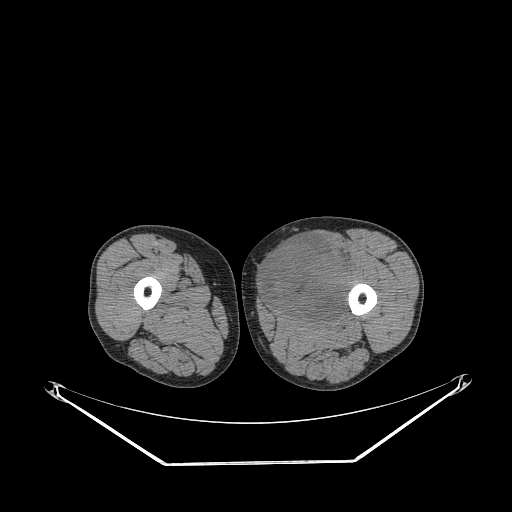
CT of an extremity soft-tissue mass (from a PET/CT study), one axial slice; position 242 of 267 along the scan axis; reconstruction kernel STANDARD; 140 kVp; soft-tissue window (W 400 / L 40 HU); 512 × 512 image matrix, field of view 500 × 500 mm. Male patient. From the clinical record (not read from this slice): histological type: pleiomorphic liposarcoma; grade: high; site of the primary tumour: left thigh.
Outlined on this slice (expert contour drawn on MRI and transferred to this co-registered scan by the dataset authors):
- gross tumour volume including surrounding oedema: bounding box <263,235,357,321> (left, top, right, bottom; pixels)
- gross tumour volume (mass): <263,235,352,321>